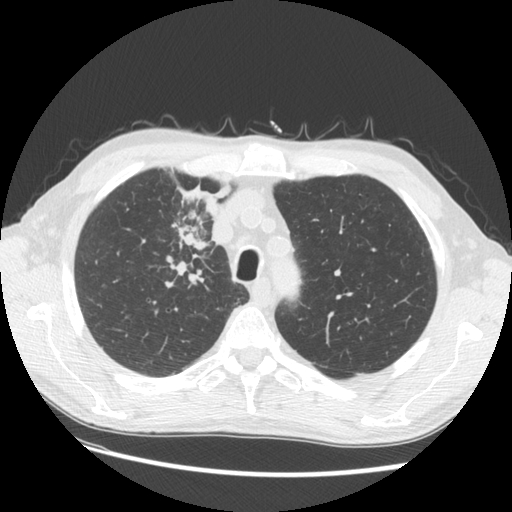
Low-dose screening chest CT, one axial slice. Slice 105 of 133 in the series (ordered by position). Lung window (W 1500 / L -600 HU). 2.5 mm slice thickness. 512 × 512 image matrix, field of view 360 × 360 mm.
Outlined on this slice (manually delineated by an expert):
- lesion 1 (tumor, hilum of right lung): bounding box (x1, y1, x2, y2) in pixels: (170, 183, 231, 250)